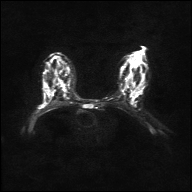
Breast MRI, one axial slice. Position 21 of 36 along the scan axis. Diffusion-weighted series; image 2 of 4 stored at this slice position (different b-values; order by instance number). 1.5 T. 4 mm slice thickness. 192 × 192 image matrix. Female patient.
Outlined on this slice (expert manual segmentation):
- tumour on diffusion-weighted imaging: bounding box <39,106,42,108> (left, top, right, bottom; pixels)